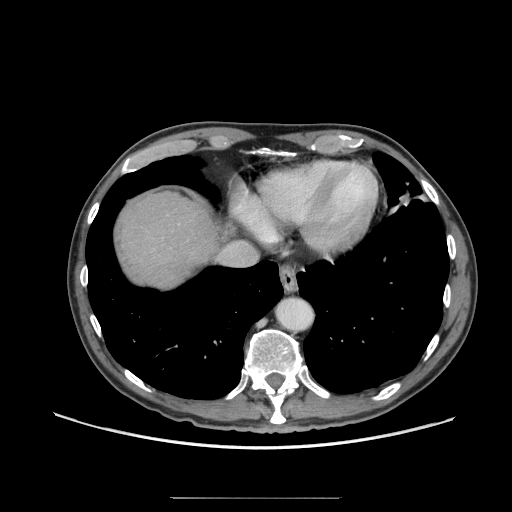
Contrast-enhanced abdominal CT (liver protocol), one axial slice; 140 kVp; soft-tissue window (W 400 / L 40 HU); 2.5 mm slice thickness; 512 × 512 image matrix. From the clinical record (not read from this slice): diagnosis: hepatocellular carcinoma (patient treated with transarterial chemoembolisation; whether this scan precedes or follows treatment is not stated here); TNM stage (as recorded): Stage-I; Child-Pugh class: A; tumour differentiation: well differentiated; tumour size: 3.5 cm.
Outlined on this slice (semi-automatically segmented with operator editing):
- abdominal aorta: bounding box <277,298,312,331> (left, top, right, bottom; pixels)
- liver parenchyma outside the tumour (the mass and vessels are separate outlines, so this box may not span the whole liver): <118,192,218,288>